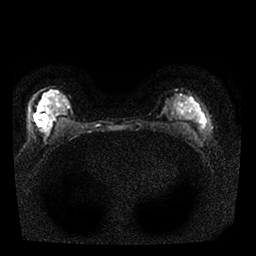
Breast MRI, one axial slice; slice 14 of 25 in the series (ordered by position); diffusion-weighted series; image 2 of 4 stored at this slice position (different b-values; order by instance number); 1.5 T; 256 × 256 image matrix, field of view 310 × 310 mm. Female patient.
Structures marked on this image (outlined manually by an expert reader):
- tumour on diffusion-weighted imaging: bounding box (x1, y1, x2, y2) in pixels: (39, 121, 50, 141)